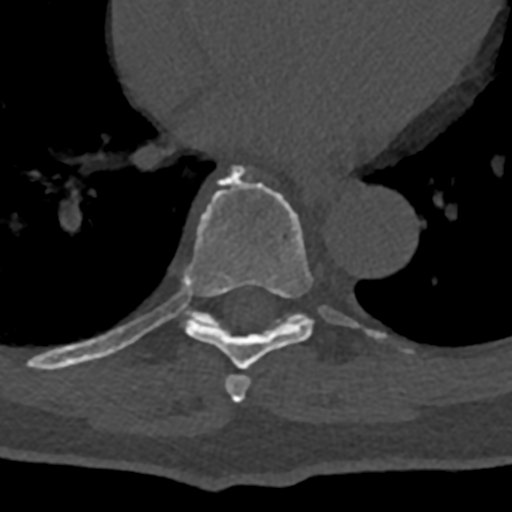
CT including the spine, one axial slice; position 700 of 797 along the scan axis; reconstruction kernel Br40s/3; 120 kVp; bone window (W 1800 / L 400 HU); 0.5 mm slice thickness; 512 × 512 image matrix. Patient: male, 74 years. From the clinical record (not read from this slice): primary cancer: renal.
Structures marked on this image (semi-automatically segmented with operator editing):
- T7 vertebra: bounding box (x1, y1, x2, y2) in pixels: (225, 374, 251, 403)
- T8 vertebra: (70, 165, 358, 370)
- T9 vertebra: (178, 292, 411, 353)